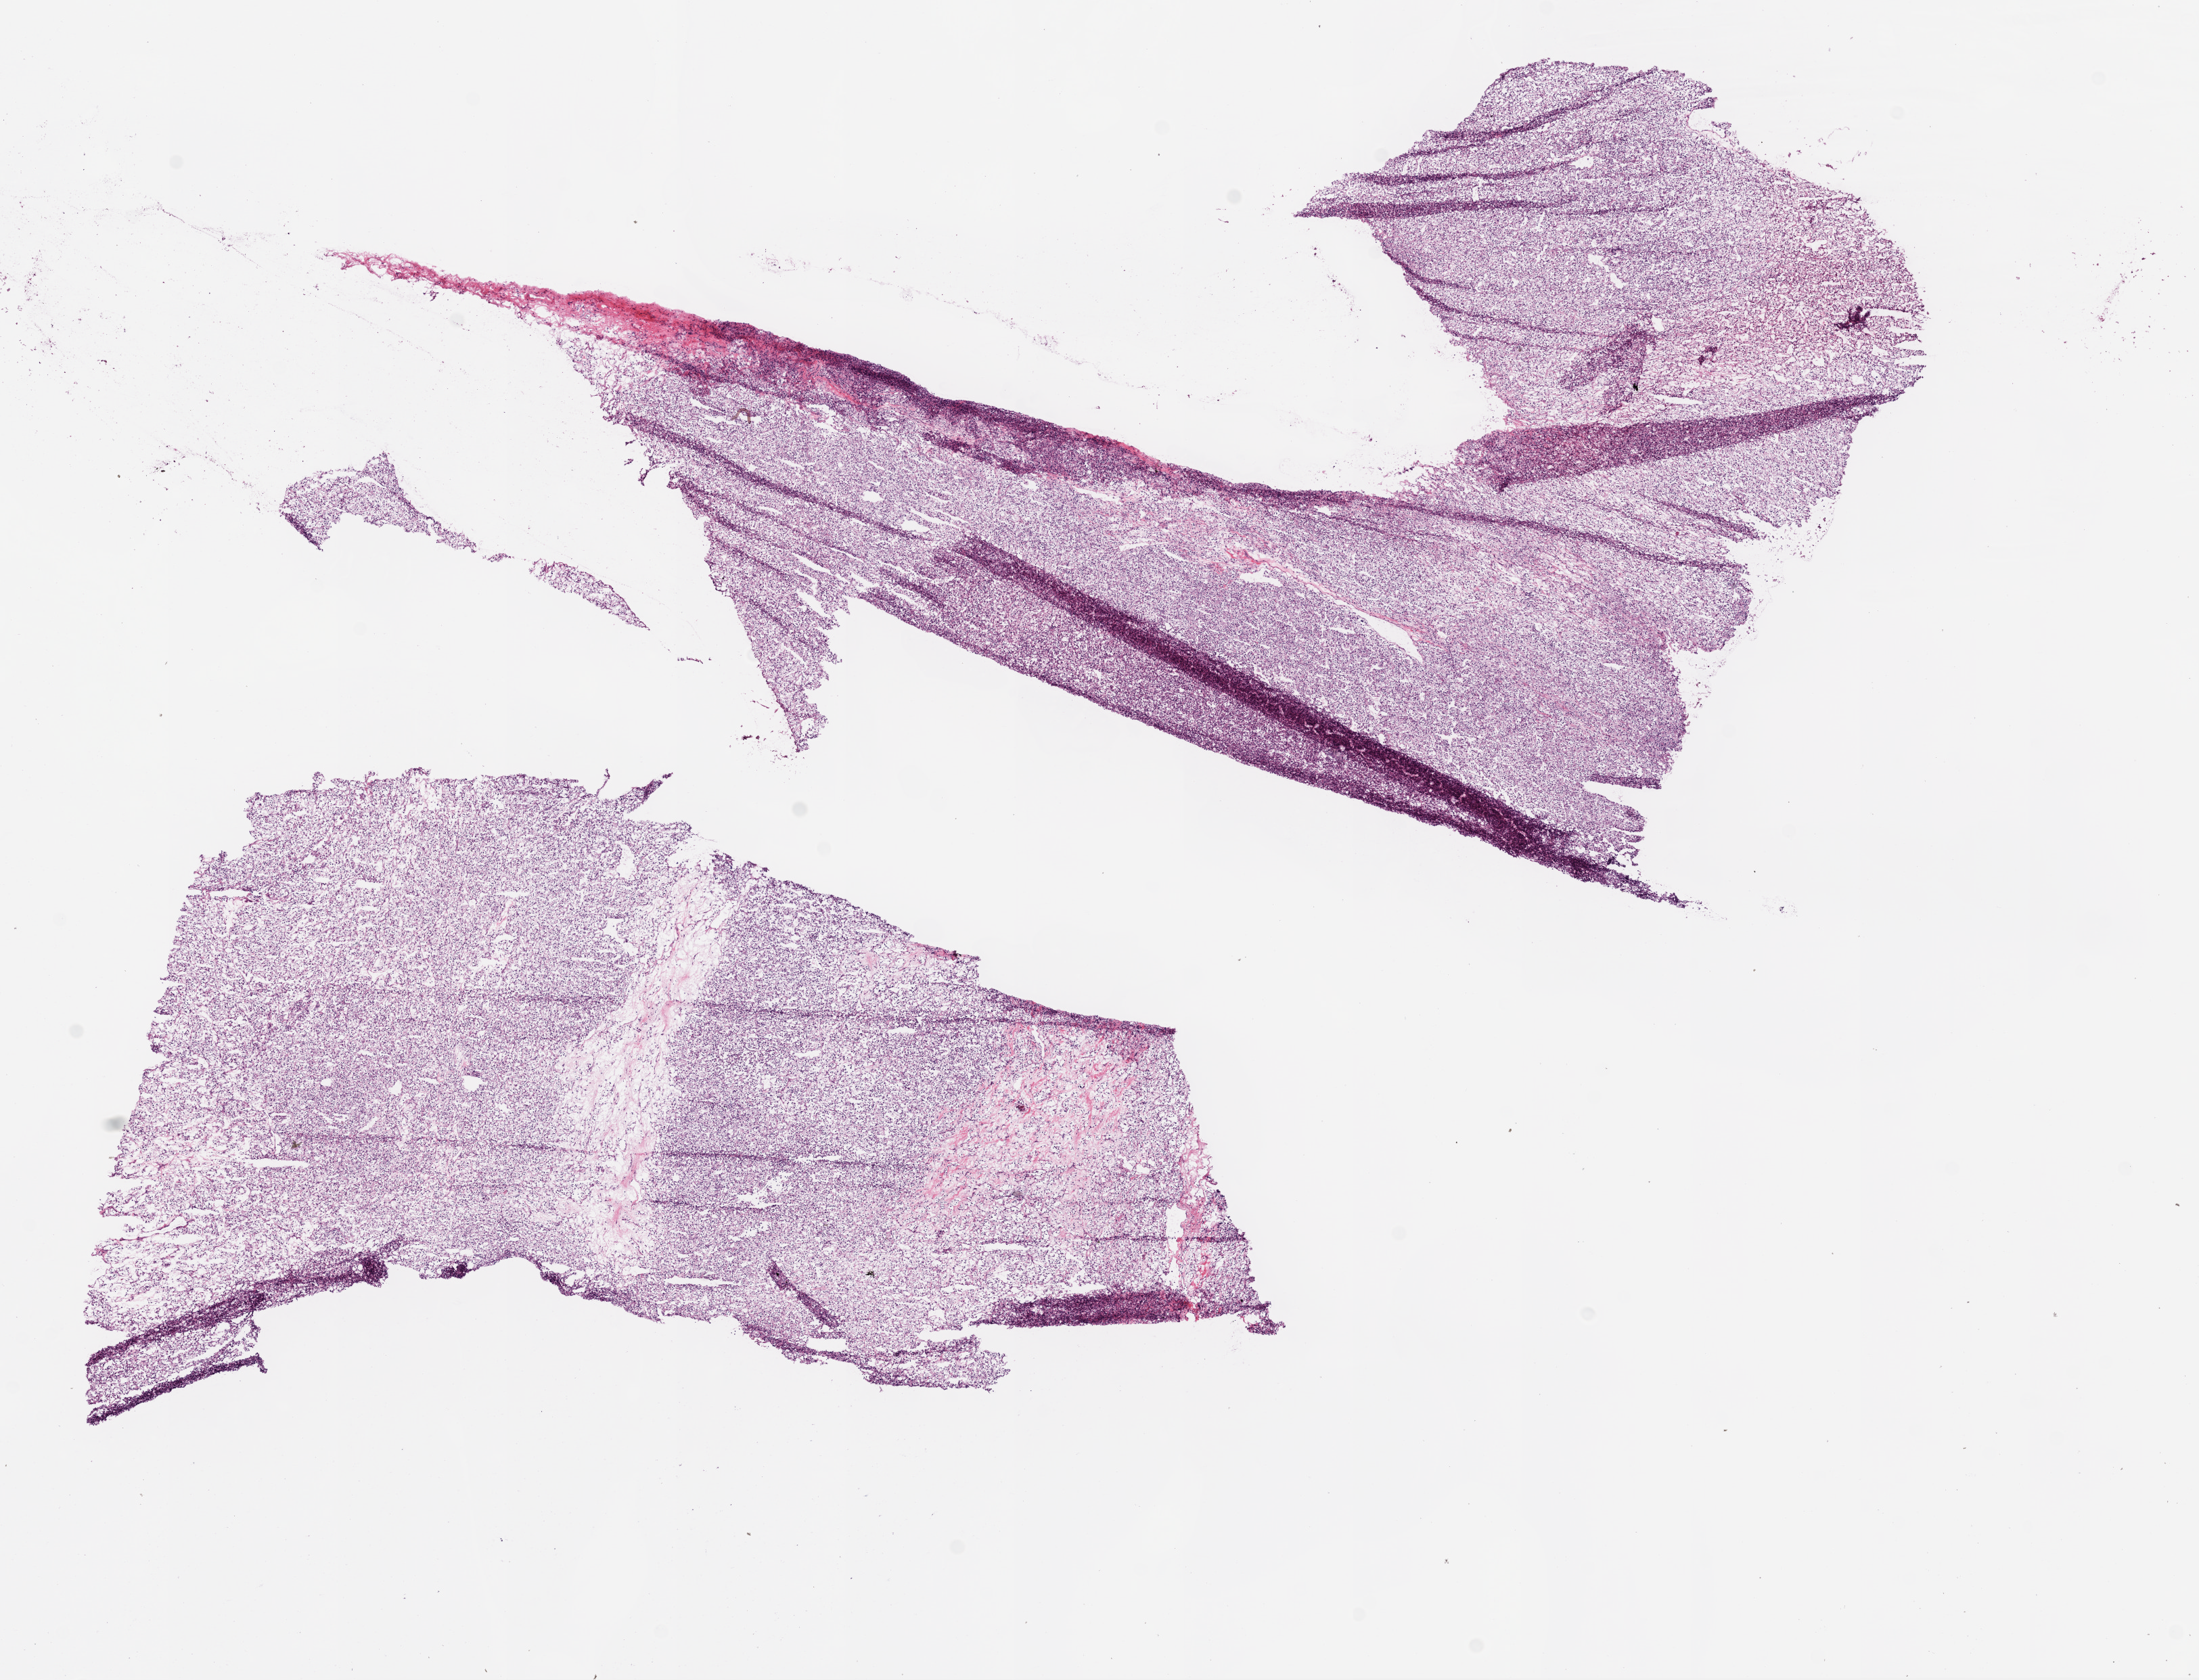
Whole-slide histology image, H&E-stained, low-resolution overview of the scanned area, about 13.0 x 10.0 mm. Frozen section. Sample: primary tumour, kidney. Male patient; age at initial diagnosis 52 years. Histologic grade: G2 (moderately differentiated). Composition of this section per pathologist review: tumour cells 90%, tumour nuclei 85%, normal cells 0%, stromal cells 10%, necrosis 0%.
Diagnosis: Clear cell adenocarcinoma, NOS. AJCC pathologic stage: I.